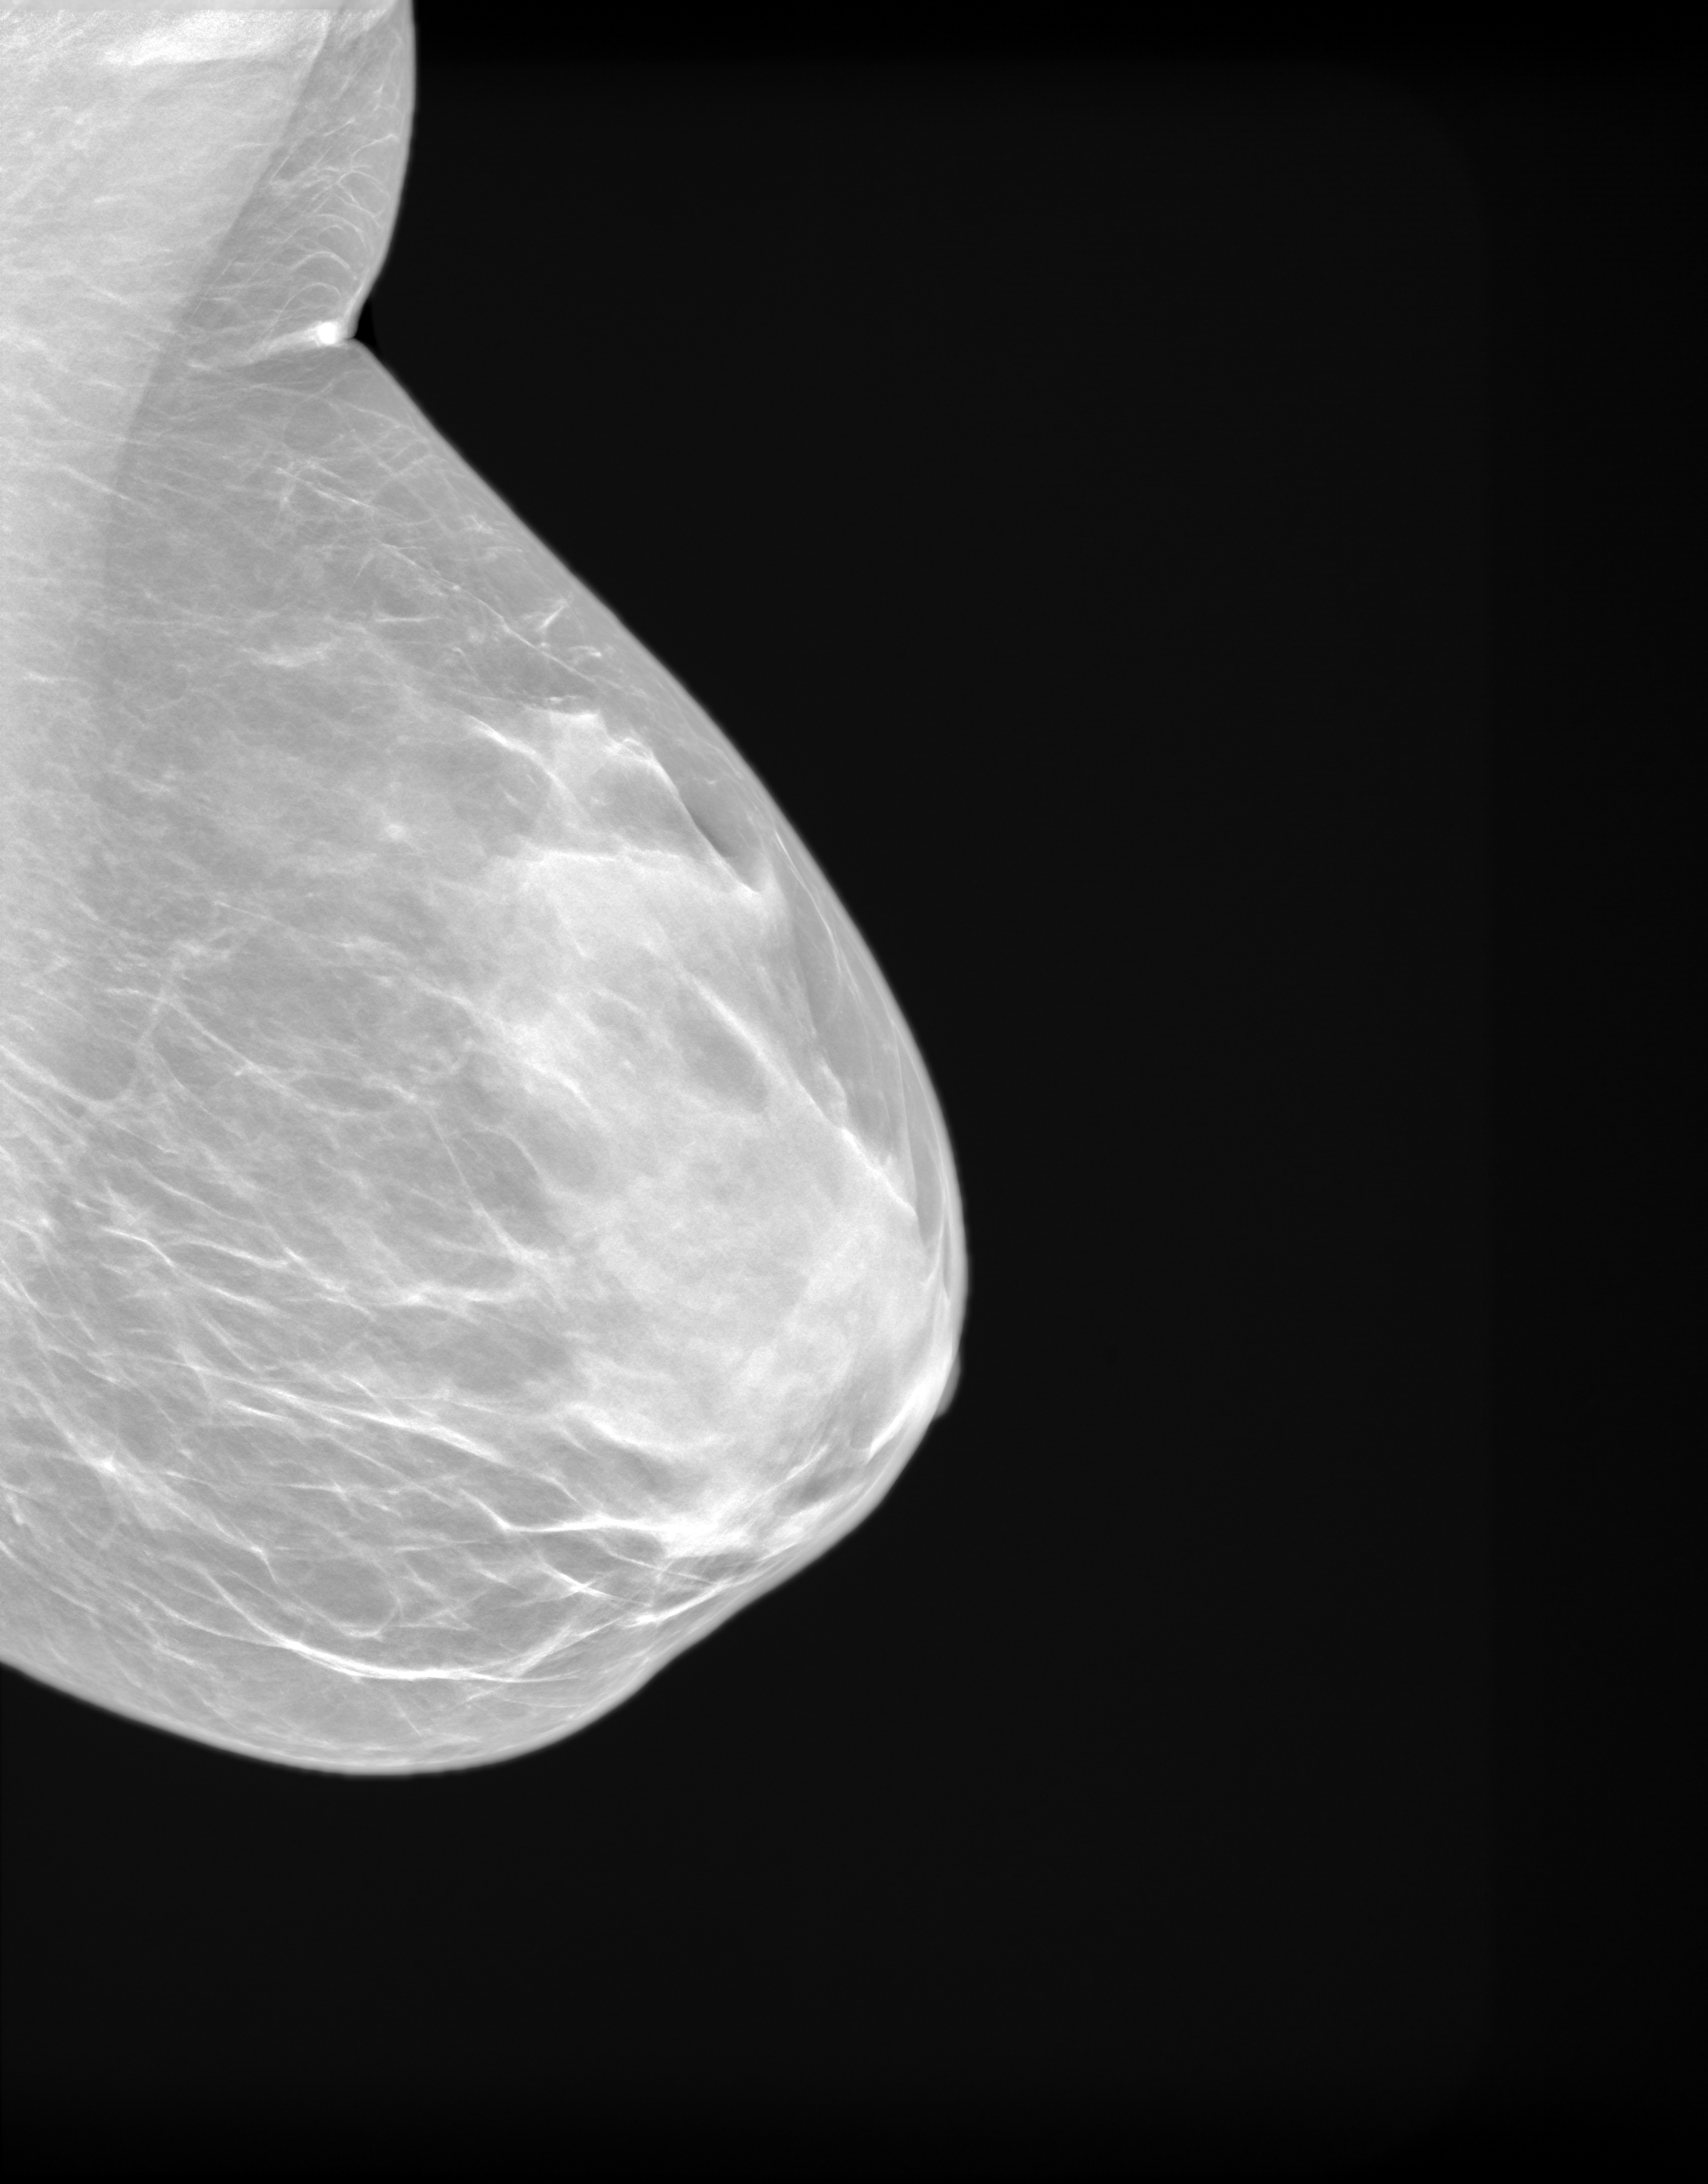
Annual screening mammography examination. Patient: female, 49 years.
Image type: synthesized 2-D view from tomosynthesis. Breast: left. Projection: MLO view.